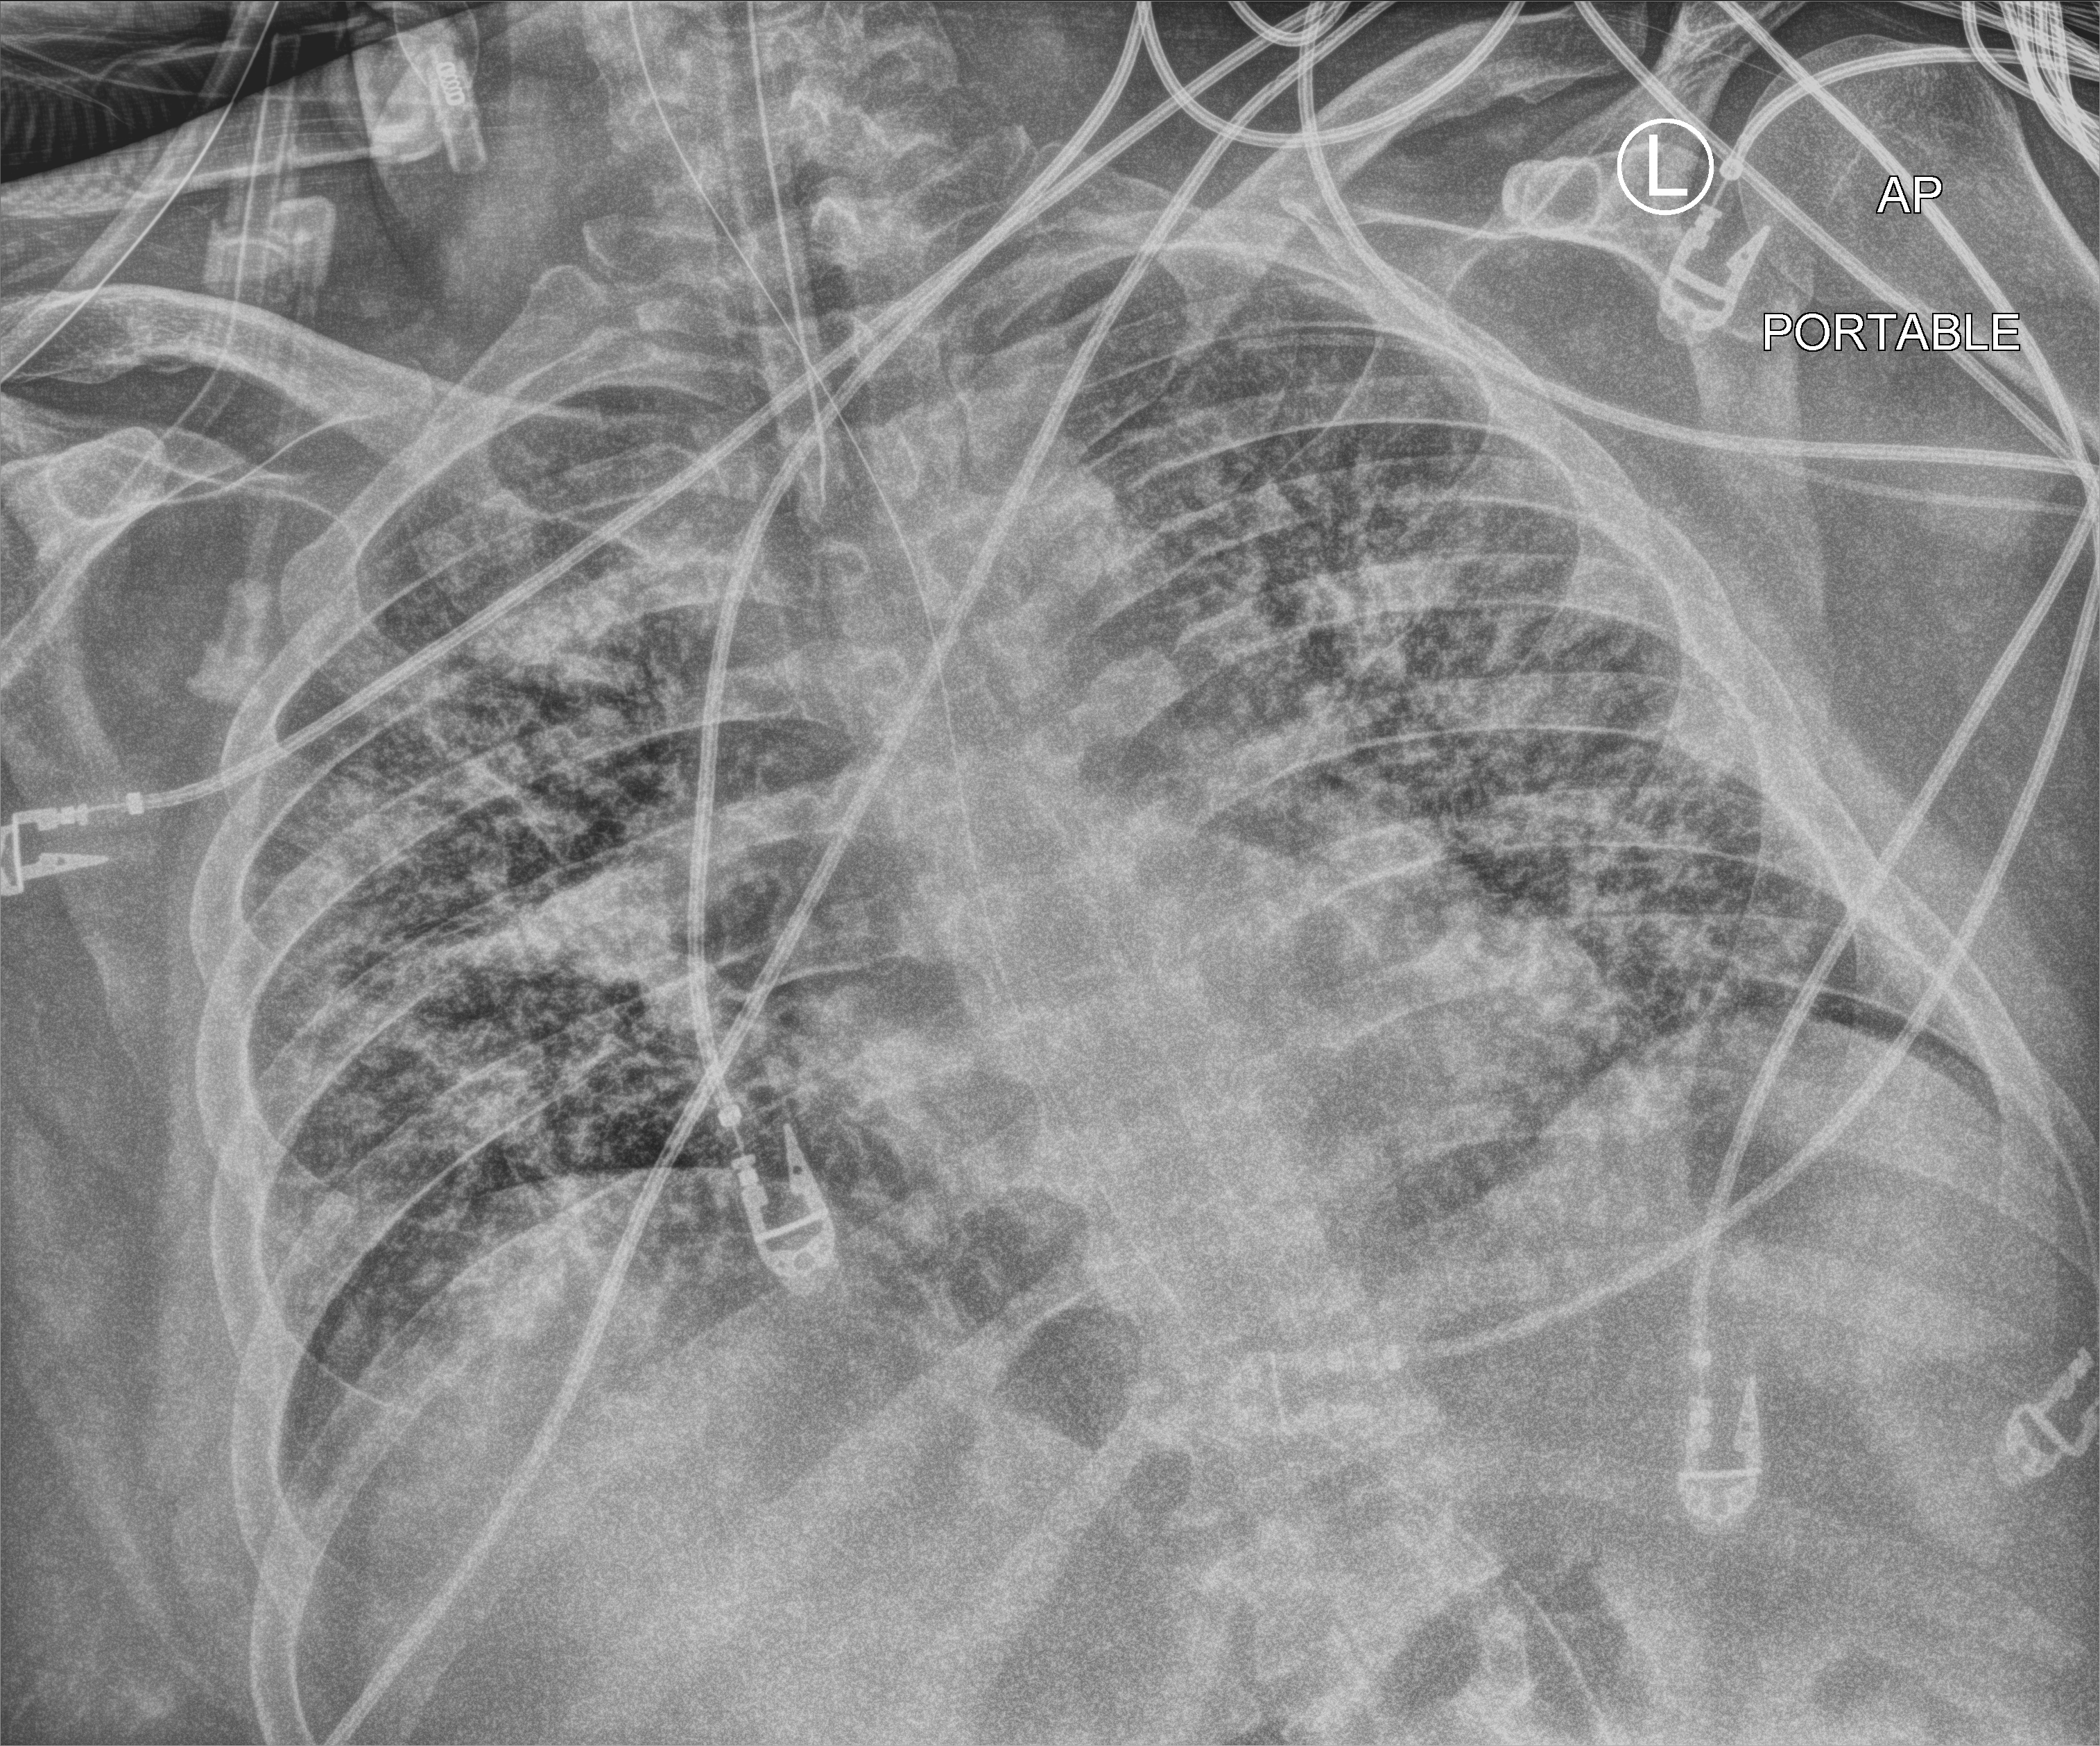
Chest X-ray (portable), anteroposterior (AP) projection. Adult patient hospitalised with COVID-19, age 18–59 years.
Admission-level facts for this patient (not findings on this image; timing relative to this image not recorded): mechanically ventilated during this hospital stay: yes; admitted to intensive care during this hospital stay: yes.